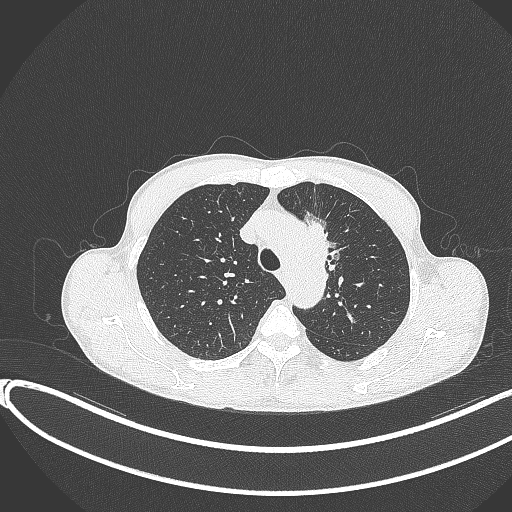
Chest CT, one axial slice; position 287 of 374 along the scan axis; 120 kVp; lung window (W 1500 / L -600 HU); 1 mm slice thickness; 512 × 512 image matrix. Patient: male, 58 years. Case-level facts recorded for this patient, not image findings: clinical TNM (as recorded): T1c N1 M0.
Structures marked on this image (rectangle marked by the reading radiologist):
- lung tumour (recorded histology: adenocarcinoma): bounding box [x1, y1, x2, y2] px = [301, 209, 345, 276]